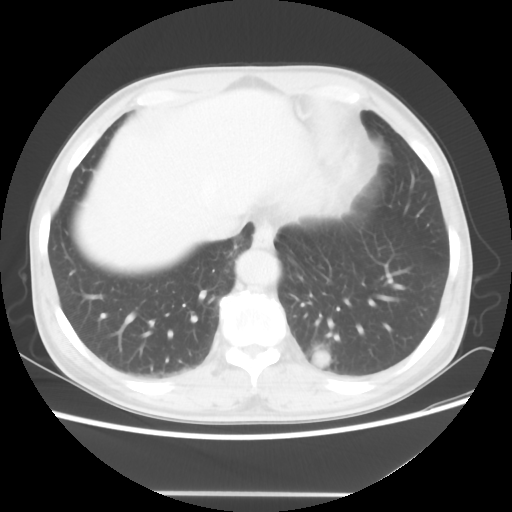
Chest CT, one axial slice. Position 13 of 60 along the scan axis. Lung window (W 1500 / L -600 HU). 512 × 512 image matrix, field of view 360 × 360 mm. Patient: male, 55 years. From the clinical record (not read from this slice): clinical TNM (as recorded): T1c N3 M0; histopathological grade: G3.
Annotated regions visible in this slice (bounding box drawn by a radiologist):
- lung tumour (recorded histology: small cell carcinoma): bounding box (x1, y1, x2, y2) in pixels: (313, 349, 334, 371)